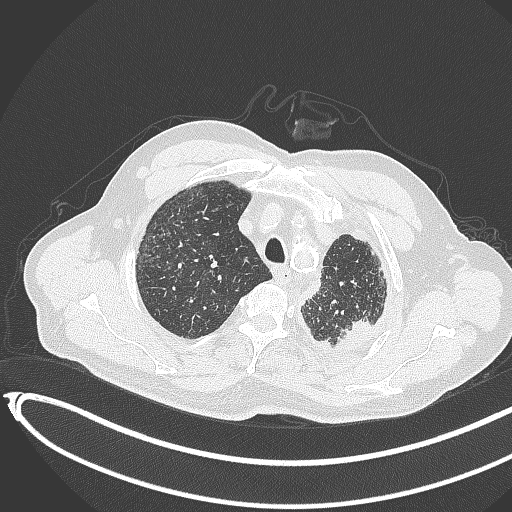
Chest CT, one axial slice; position 358 of 451 along the scan axis; reconstruction kernel B70f; 120 kVp; lung window (W 1500 / L -600 HU); 512 × 512 image matrix, field of view 400 × 400 mm. Patient: male, 78 years. Case-level facts recorded for this patient, not image findings: clinical TNM (as recorded): T1c N0 M1.
Annotated regions visible in this slice (rectangle marked by the reading radiologist):
- lung tumour (recorded histology: adenocarcinoma): bounding box [x1, y1, x2, y2] px = [335, 318, 376, 356]